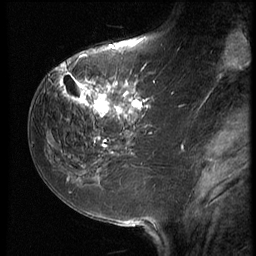
Breast MRI (dynamic contrast-enhanced), one sagittal slice; position 23 of 64 along the scan axis; 3 images stored at this slice position (order not interpretable as contrast timing); 1.5 T; TE 4.2 ms, TR 9 ms; 256 × 256 image matrix, field of view 180 × 180 mm. Female patient, age 59 years. From the clinical record (not read from this slice): setting: breast cancer imaged before/during neoadjuvant chemotherapy; receptor status: HER2-positive.
Annotated regions visible in this slice (semi-automatic segmentation, software-assisted and operator-edited):
- analysis volume of interest (the breast-tissue region the enhancement analysis was run in; not a lesion): bounding box (x1, y1, x2, y2) in pixels: (54, 65, 155, 132)
- tumour enhancement mask (voxels above the 140 % enhancement threshold inside the analysis volume of interest): (58, 65, 155, 129)